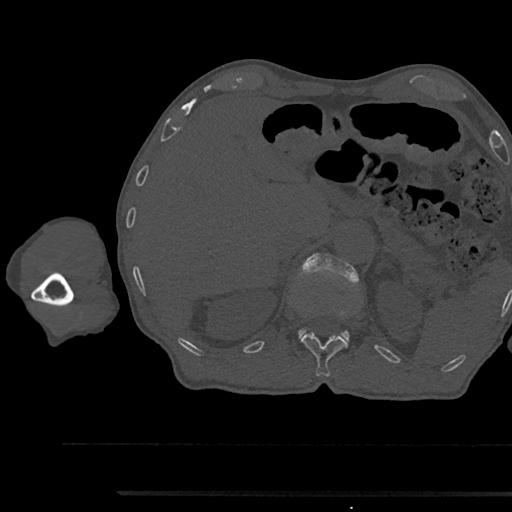
CT including the spine, one axial slice; position 686 of 797 along the scan axis; reconstruction kernel Br40s/3; 120 kVp; bone window (W 1800 / L 400 HU); 0.5 mm slice thickness; 512 × 512 image matrix, field of view 367 × 367 mm. Male patient, age 79 years. Case-level facts recorded for this patient, not image findings: primary cancer: prostate.
Structures marked on this image (semi-automatically segmented with operator editing):
- L1 vertebra: bounding box (x1, y1, x2, y2) in pixels: (297, 254, 359, 342)
- T12 vertebra: (301, 333, 349, 377)